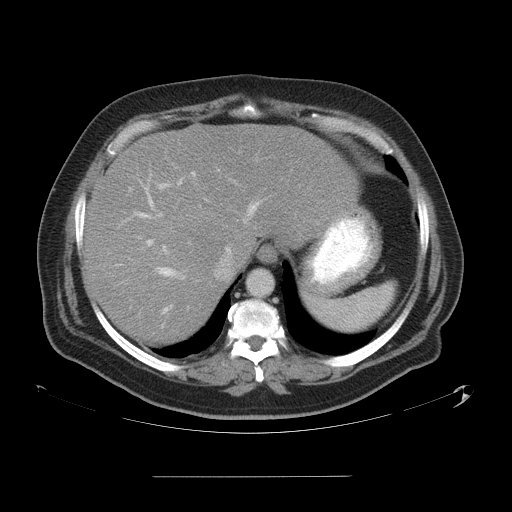
Contrast-enhanced abdominal CT, one axial slice. Position 43 of 58 along the scan axis. 120 kVp. Intravenous contrast given. Soft-tissue window (W 400 / L 40 HU). 5 mm slice thickness. 512 × 512 image matrix, field of view 480 × 480 mm. Male patient, age 63 years. From the clinical record (not read from this slice): diagnosis: colorectal cancer liver metastases, imaged before liver resection; multiple liver metastases: no; largest metastasis: 4.2 cm; disease in both lobes: no.
Structures marked on this image (outlined manually by an expert reader):
- hepatic veins: box from (x=134, y=184) to (x=261, y=313) px
- liver: (x=84, y=125)–(x=354, y=344)
- planned liver remnant (the part of the liver to remain after resection): (x=84, y=197)–(x=224, y=345)
- portal vein (with intrahepatic branches): (x=116, y=169)–(x=220, y=266)